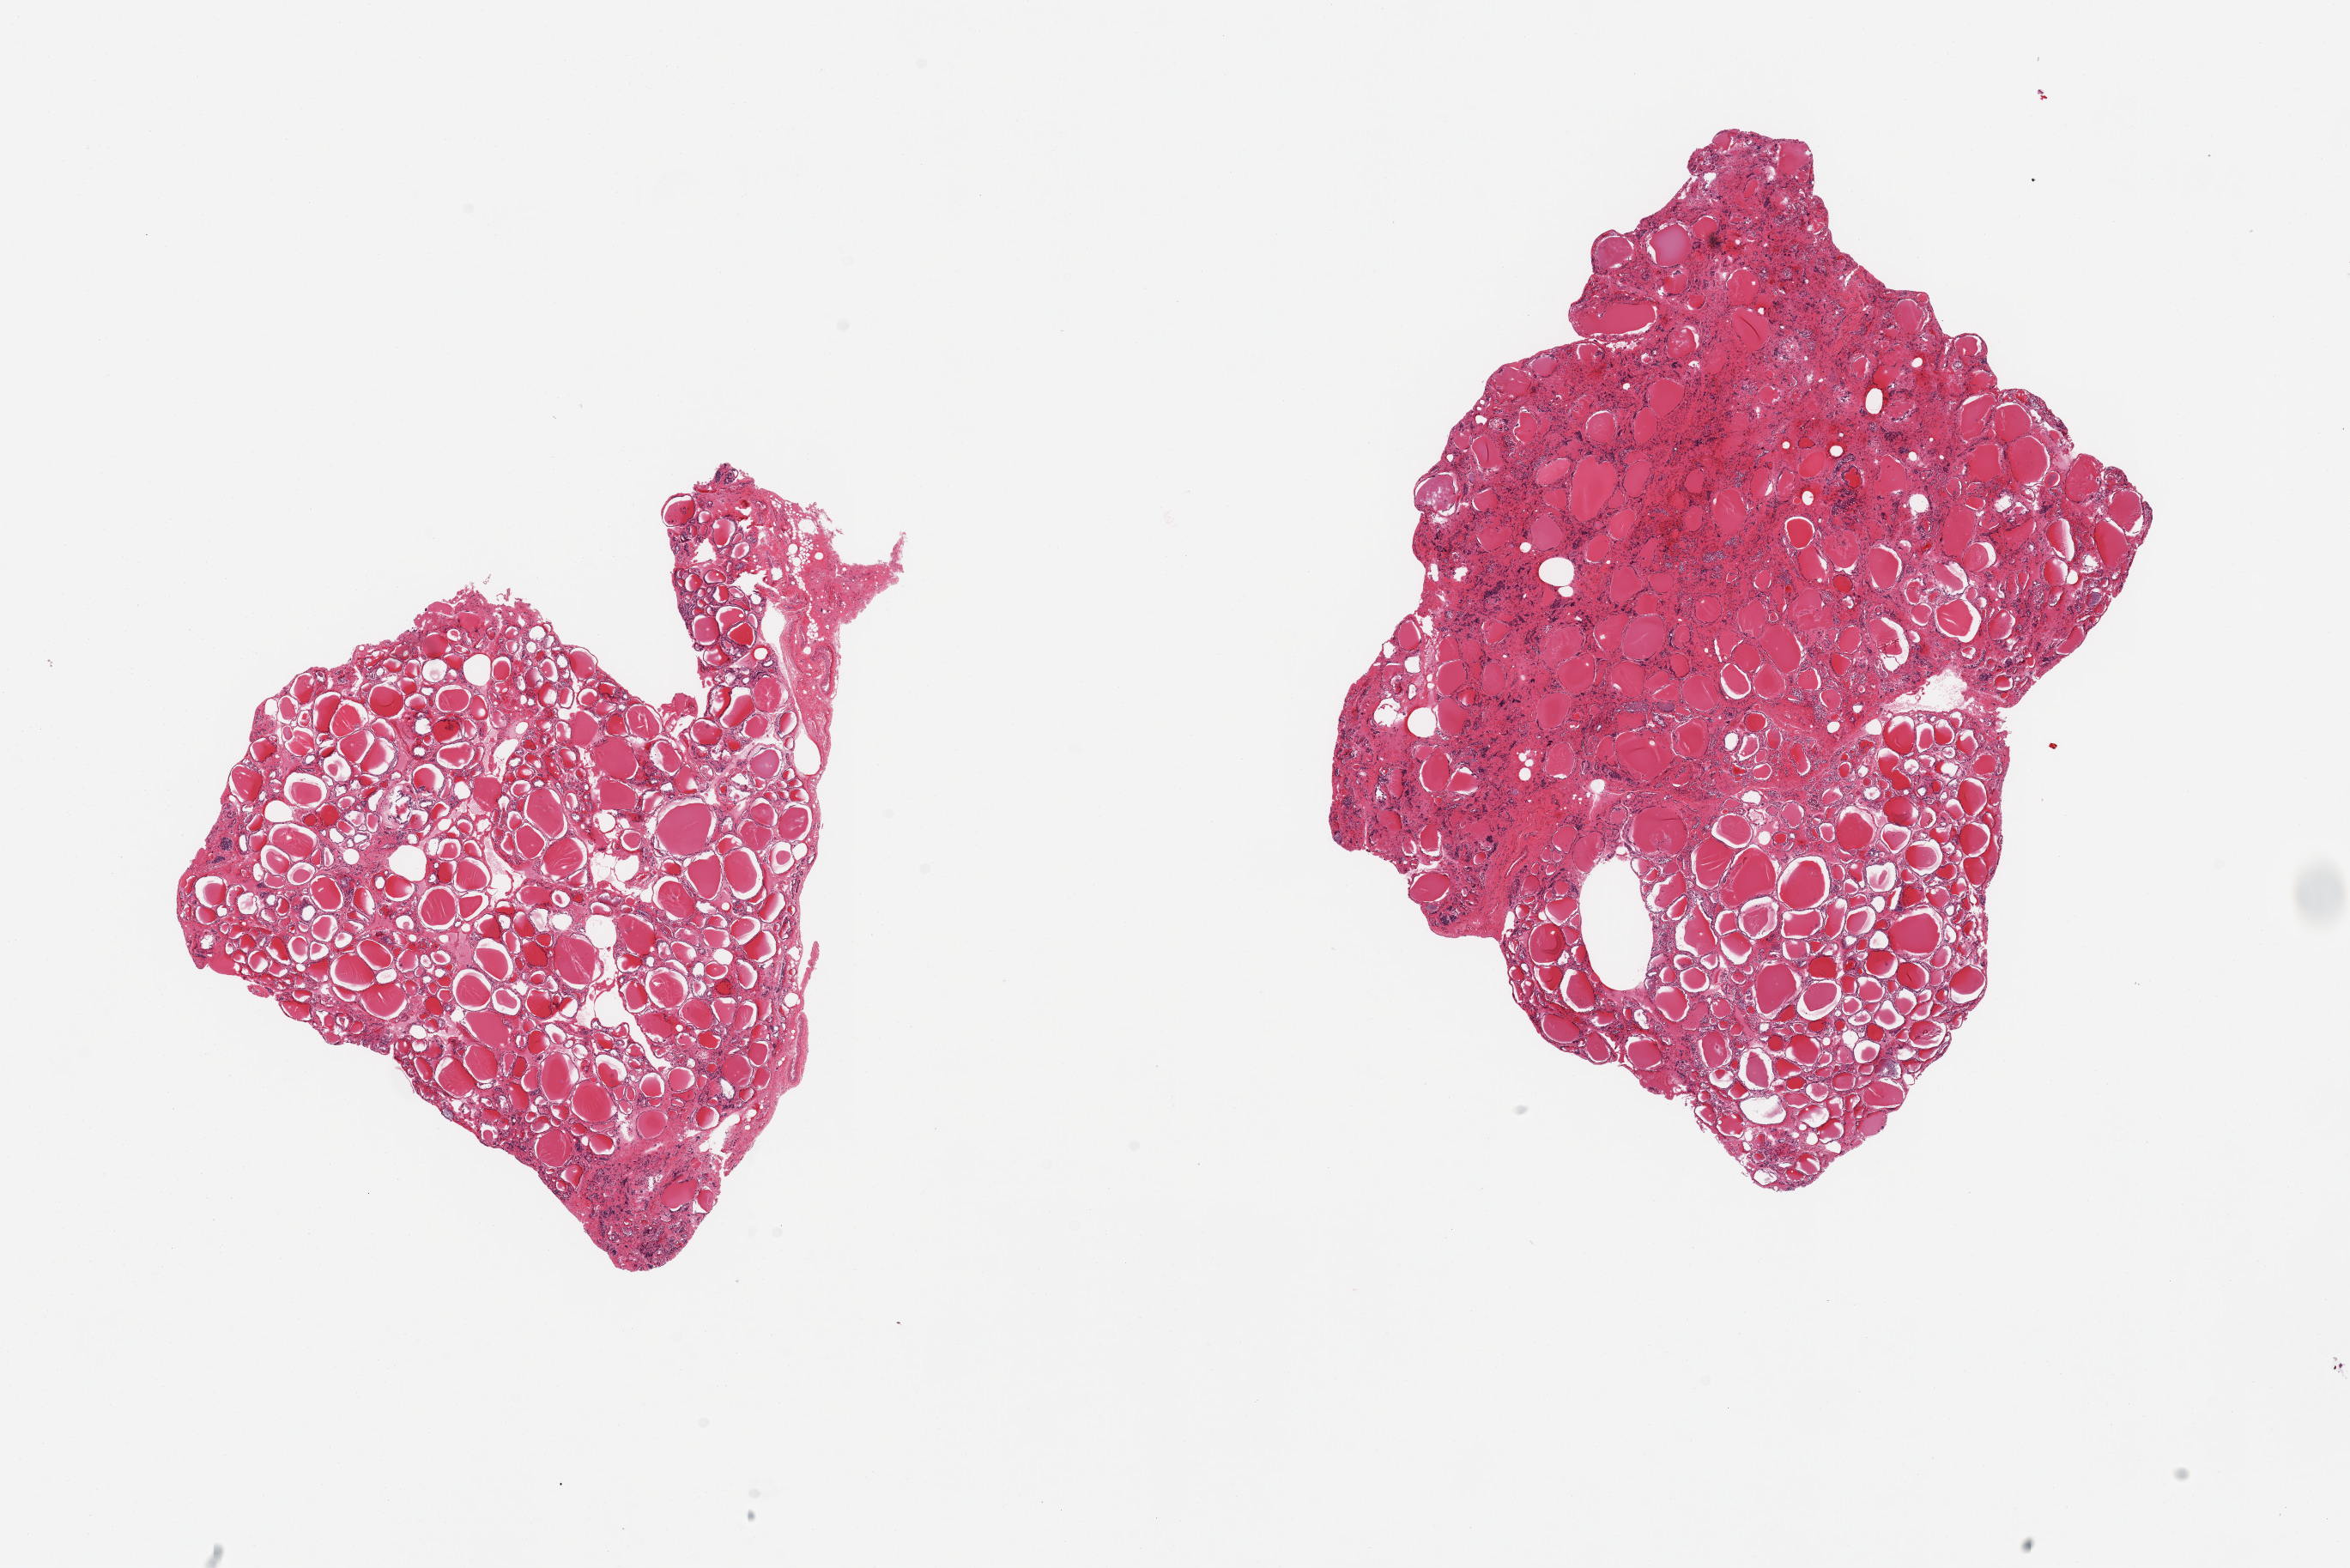
Whole-slide image, H&E stain, low-resolution overview of the scanned area, about 21.7 x 14.5 mm, PAXgene-fixed, paraffin-embedded tissue, target tissue: thyroid, donor tissue sample. Female donor.
Reviewer comment on this tissue sample: 2 pieces; 1 piece is partially traumatized.